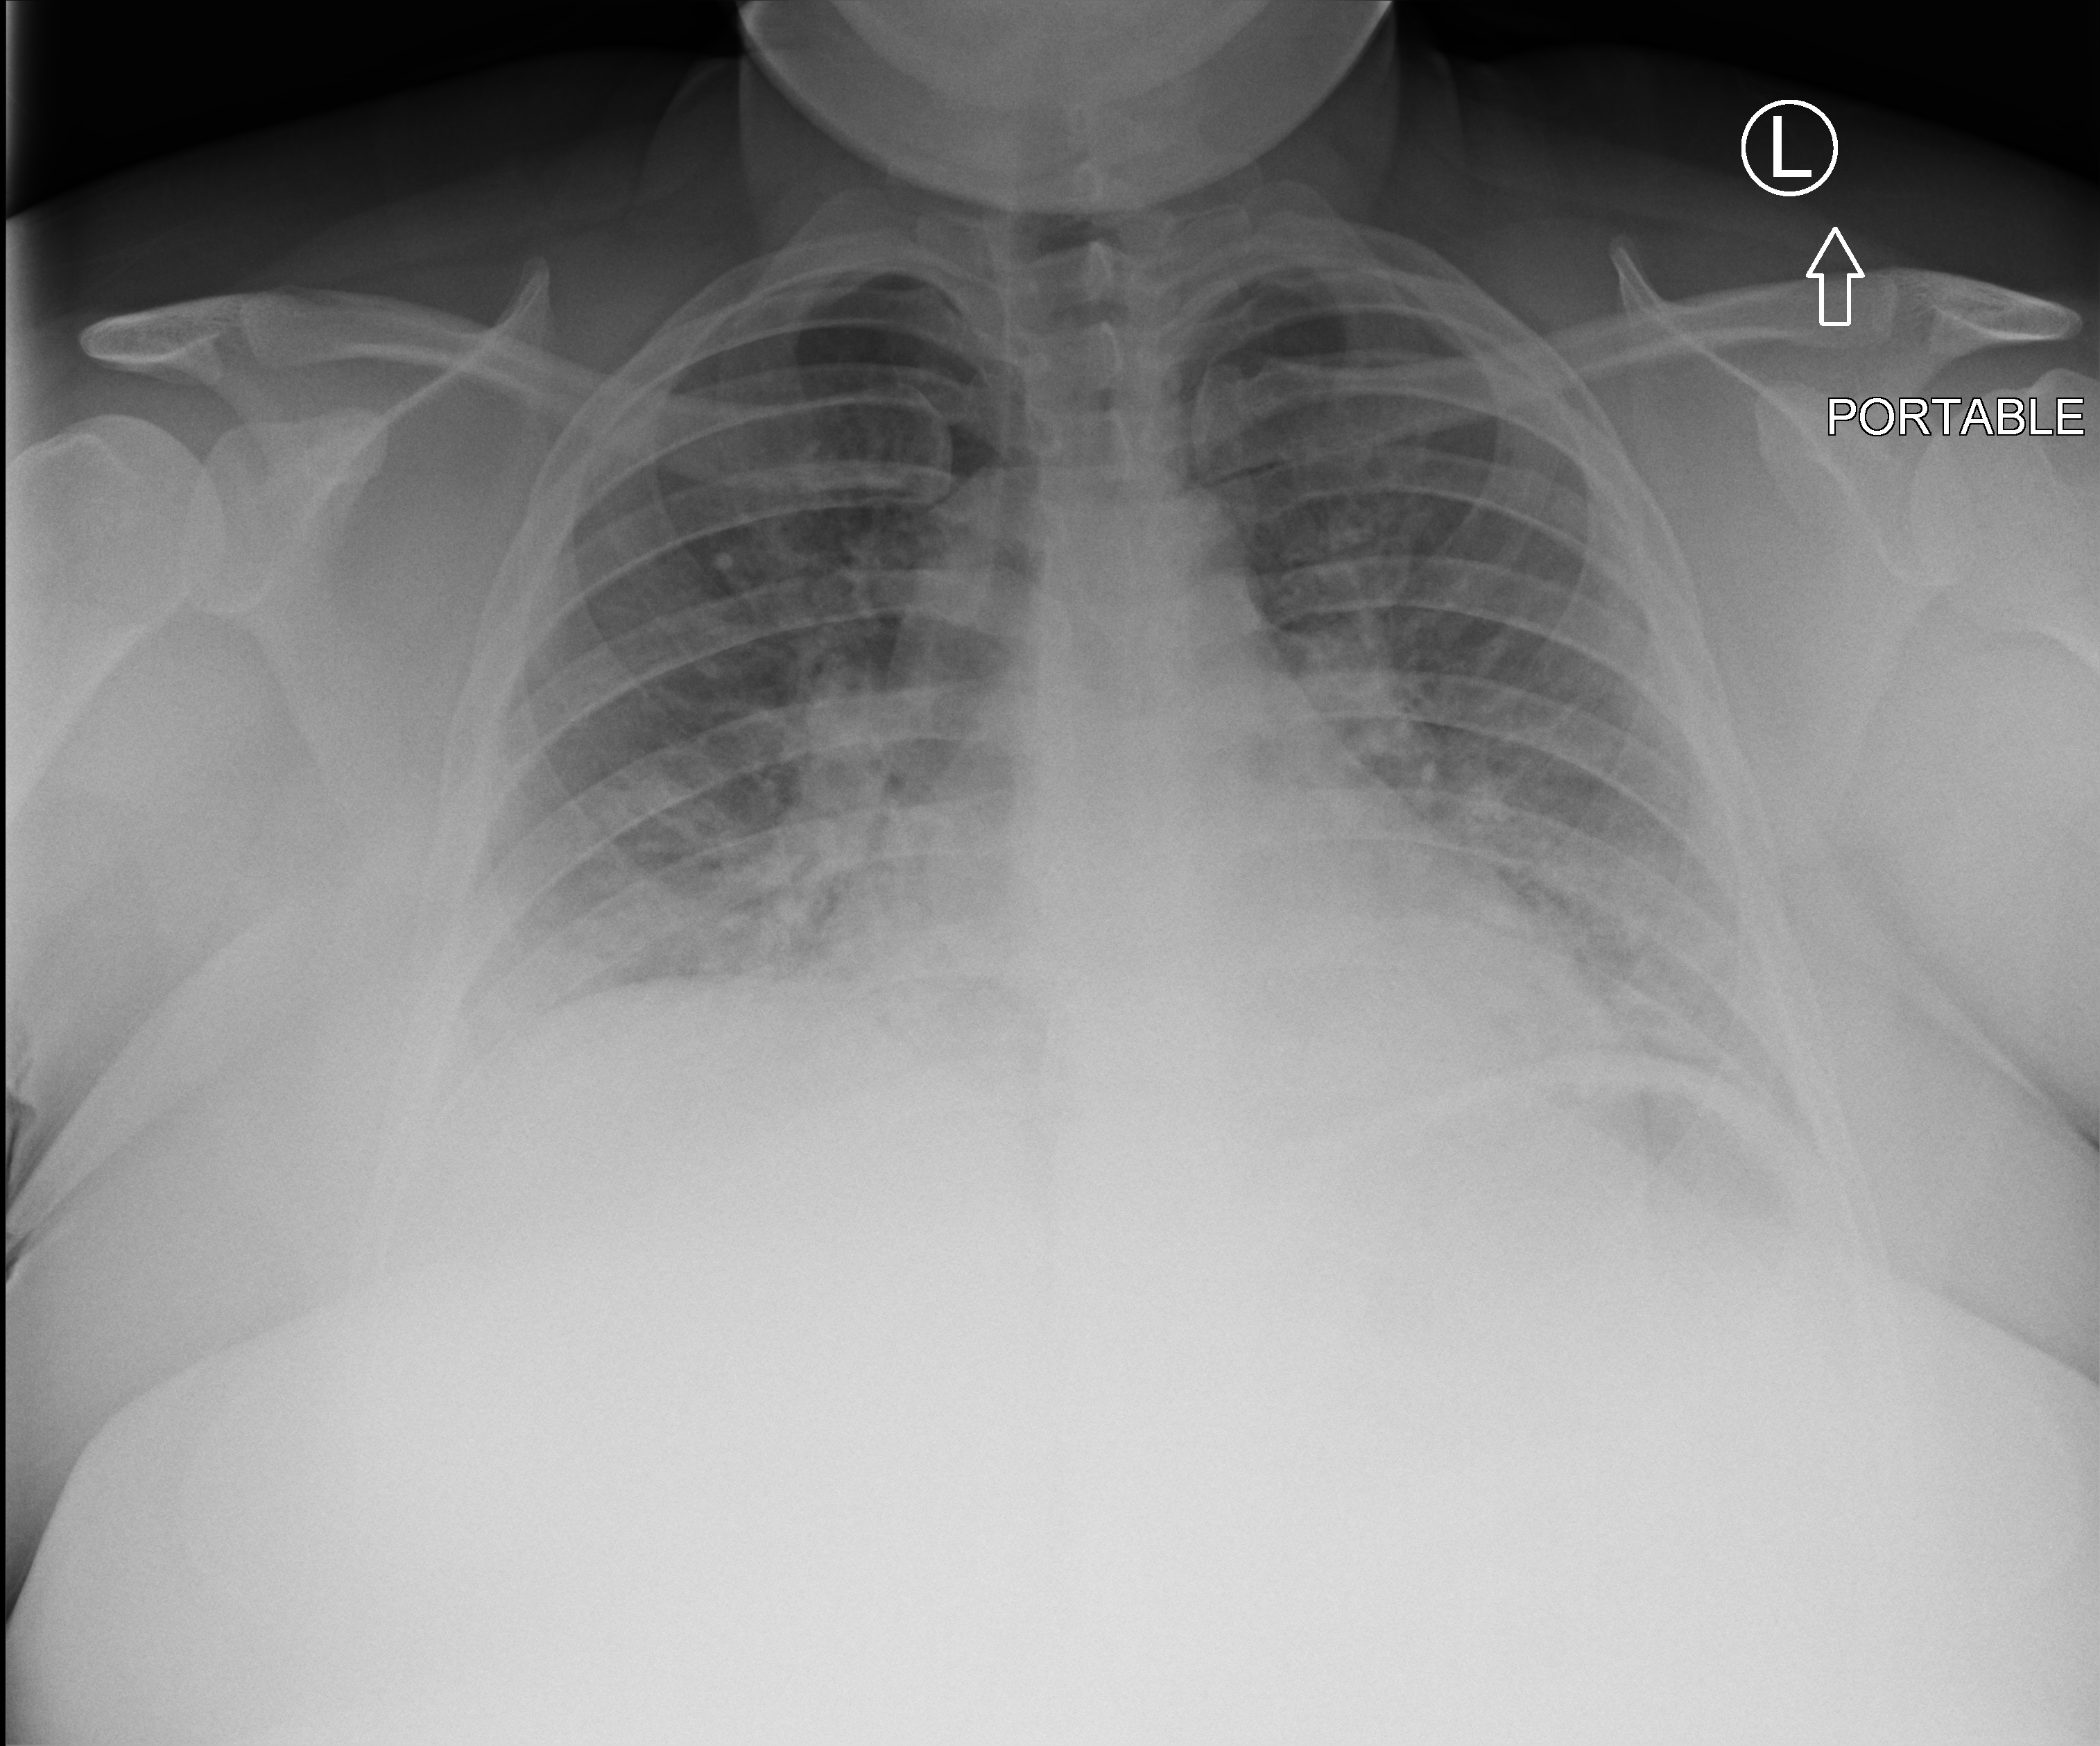
Portable chest radiograph; anteroposterior (AP) projection. Patient hospitalised with COVID-19; female, aged 18–59 years.
Hospital-stay facts (about this admission, not read from this image; timing relative to this image not recorded):
- admitted to intensive care during this hospital stay: no
- mechanically ventilated during this hospital stay: no
- COPD (admission record): no